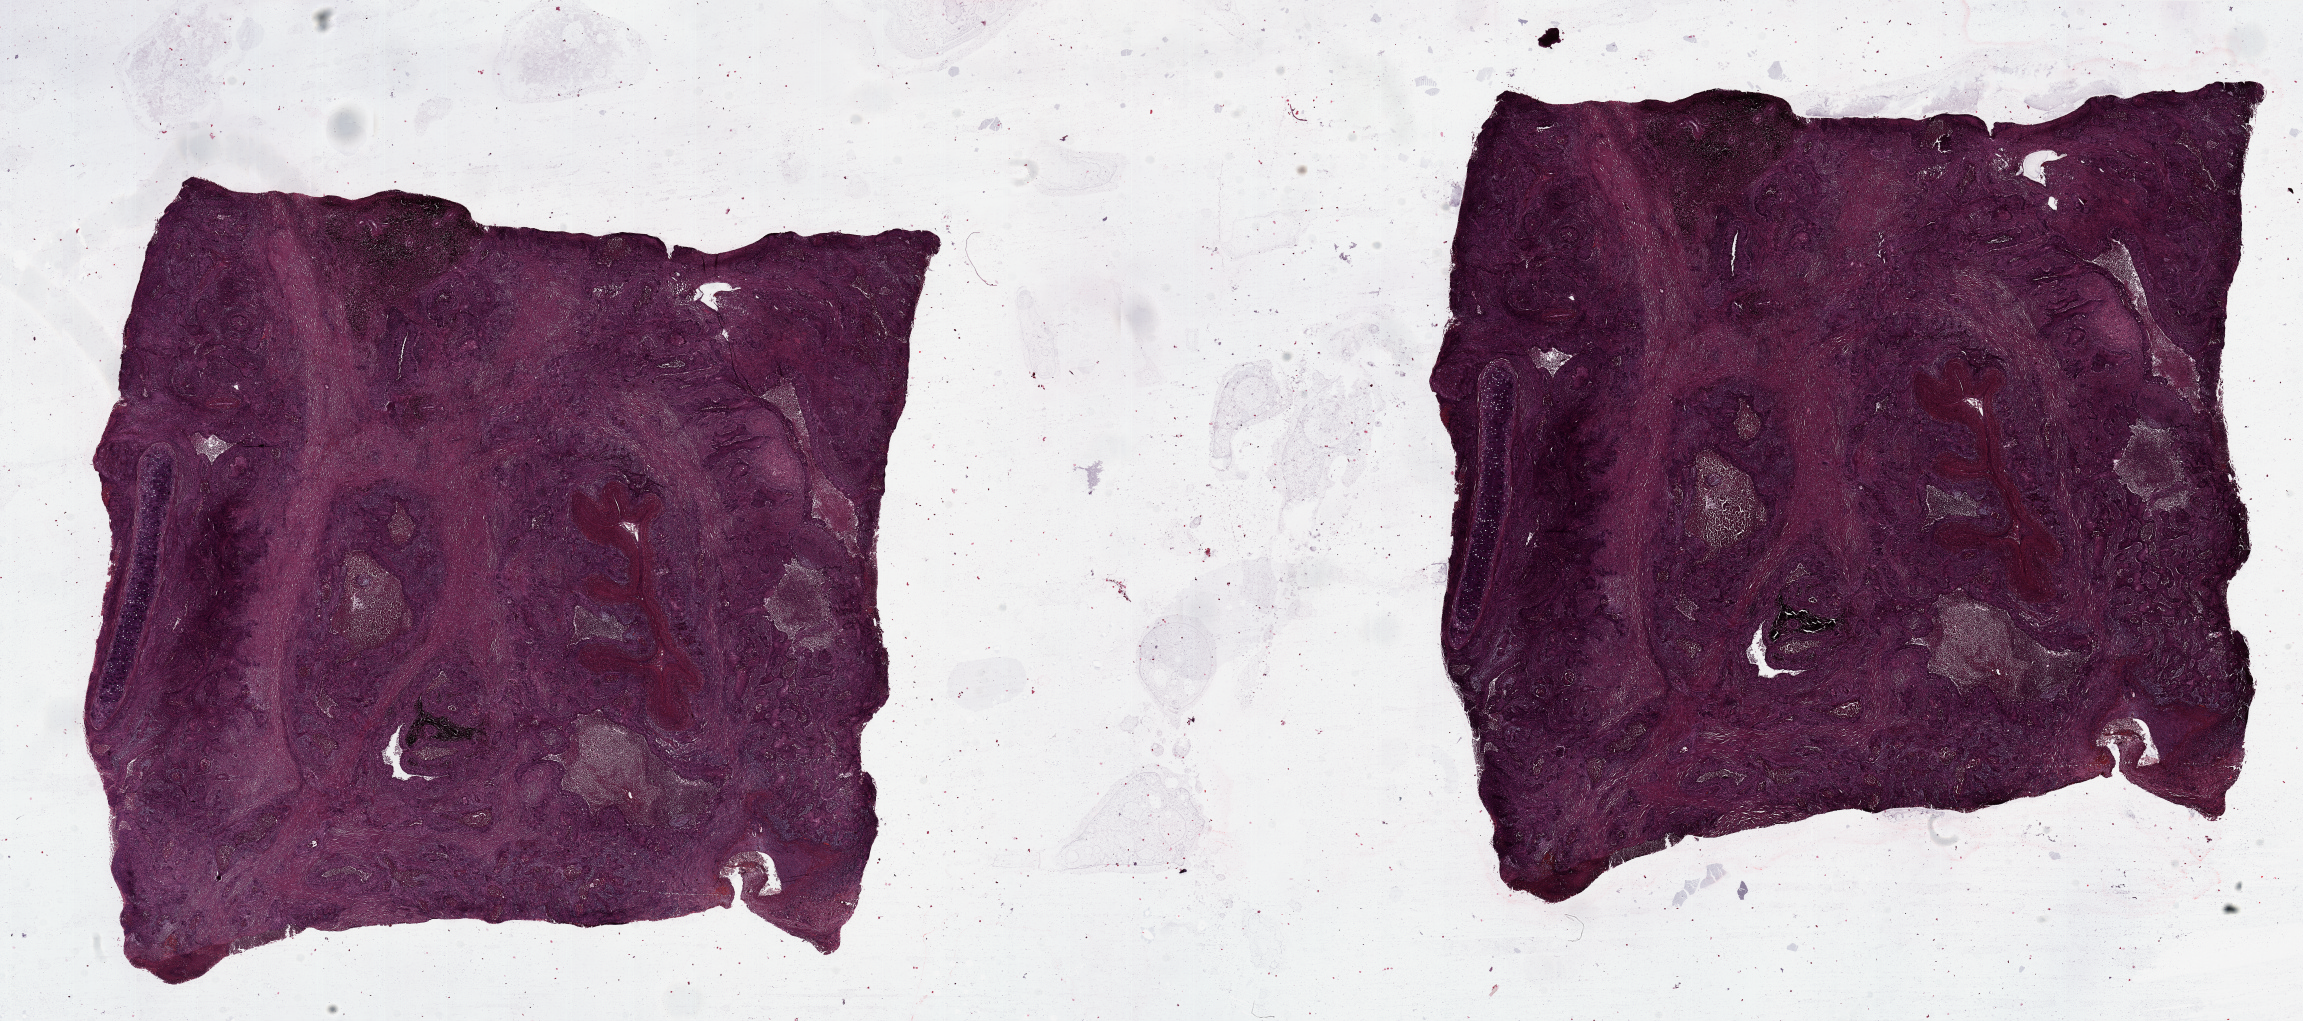
Whole-slide histology image, H&E-stained — a low-resolution overview of the entire scanned area, about 36.4 x 16.1 mm, tumour tissue sample, sampled site: lung. Patient: male, age 66 years. Histologic grade: G1 (well differentiated). Composition of this section per pathologist review: tumour nuclei 75%, necrosis 8%.
* AJCC pathologic stage: II
* diagnosis: Squamous cell carcinoma, NOS